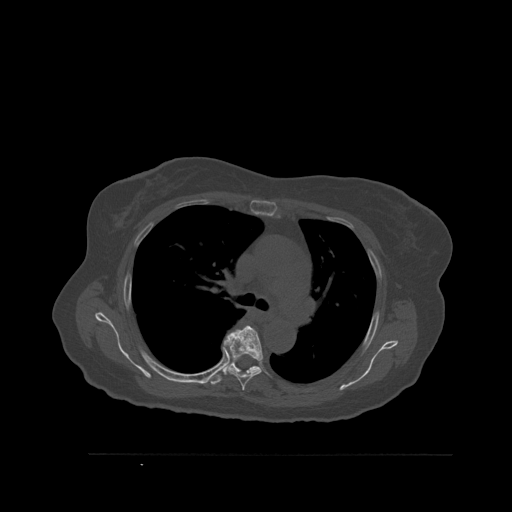
CT including the spine, one axial slice; slice 390 of 527 in the series (ordered by position); bone window (W 1800 / L 400 HU); 1.5 mm slice thickness; 512 × 512 image matrix, field of view 470 × 470 mm. Patient: female, 73 years. From the clinical record (not read from this slice): primary cancer: breast.
Structures marked on this image (semi-automatic segmentation, software-assisted and operator-edited):
- T5 vertebra: bounding box (x1, y1, x2, y2) in pixels: (224, 325, 263, 391)
- T6 vertebra: (208, 330, 262, 385)